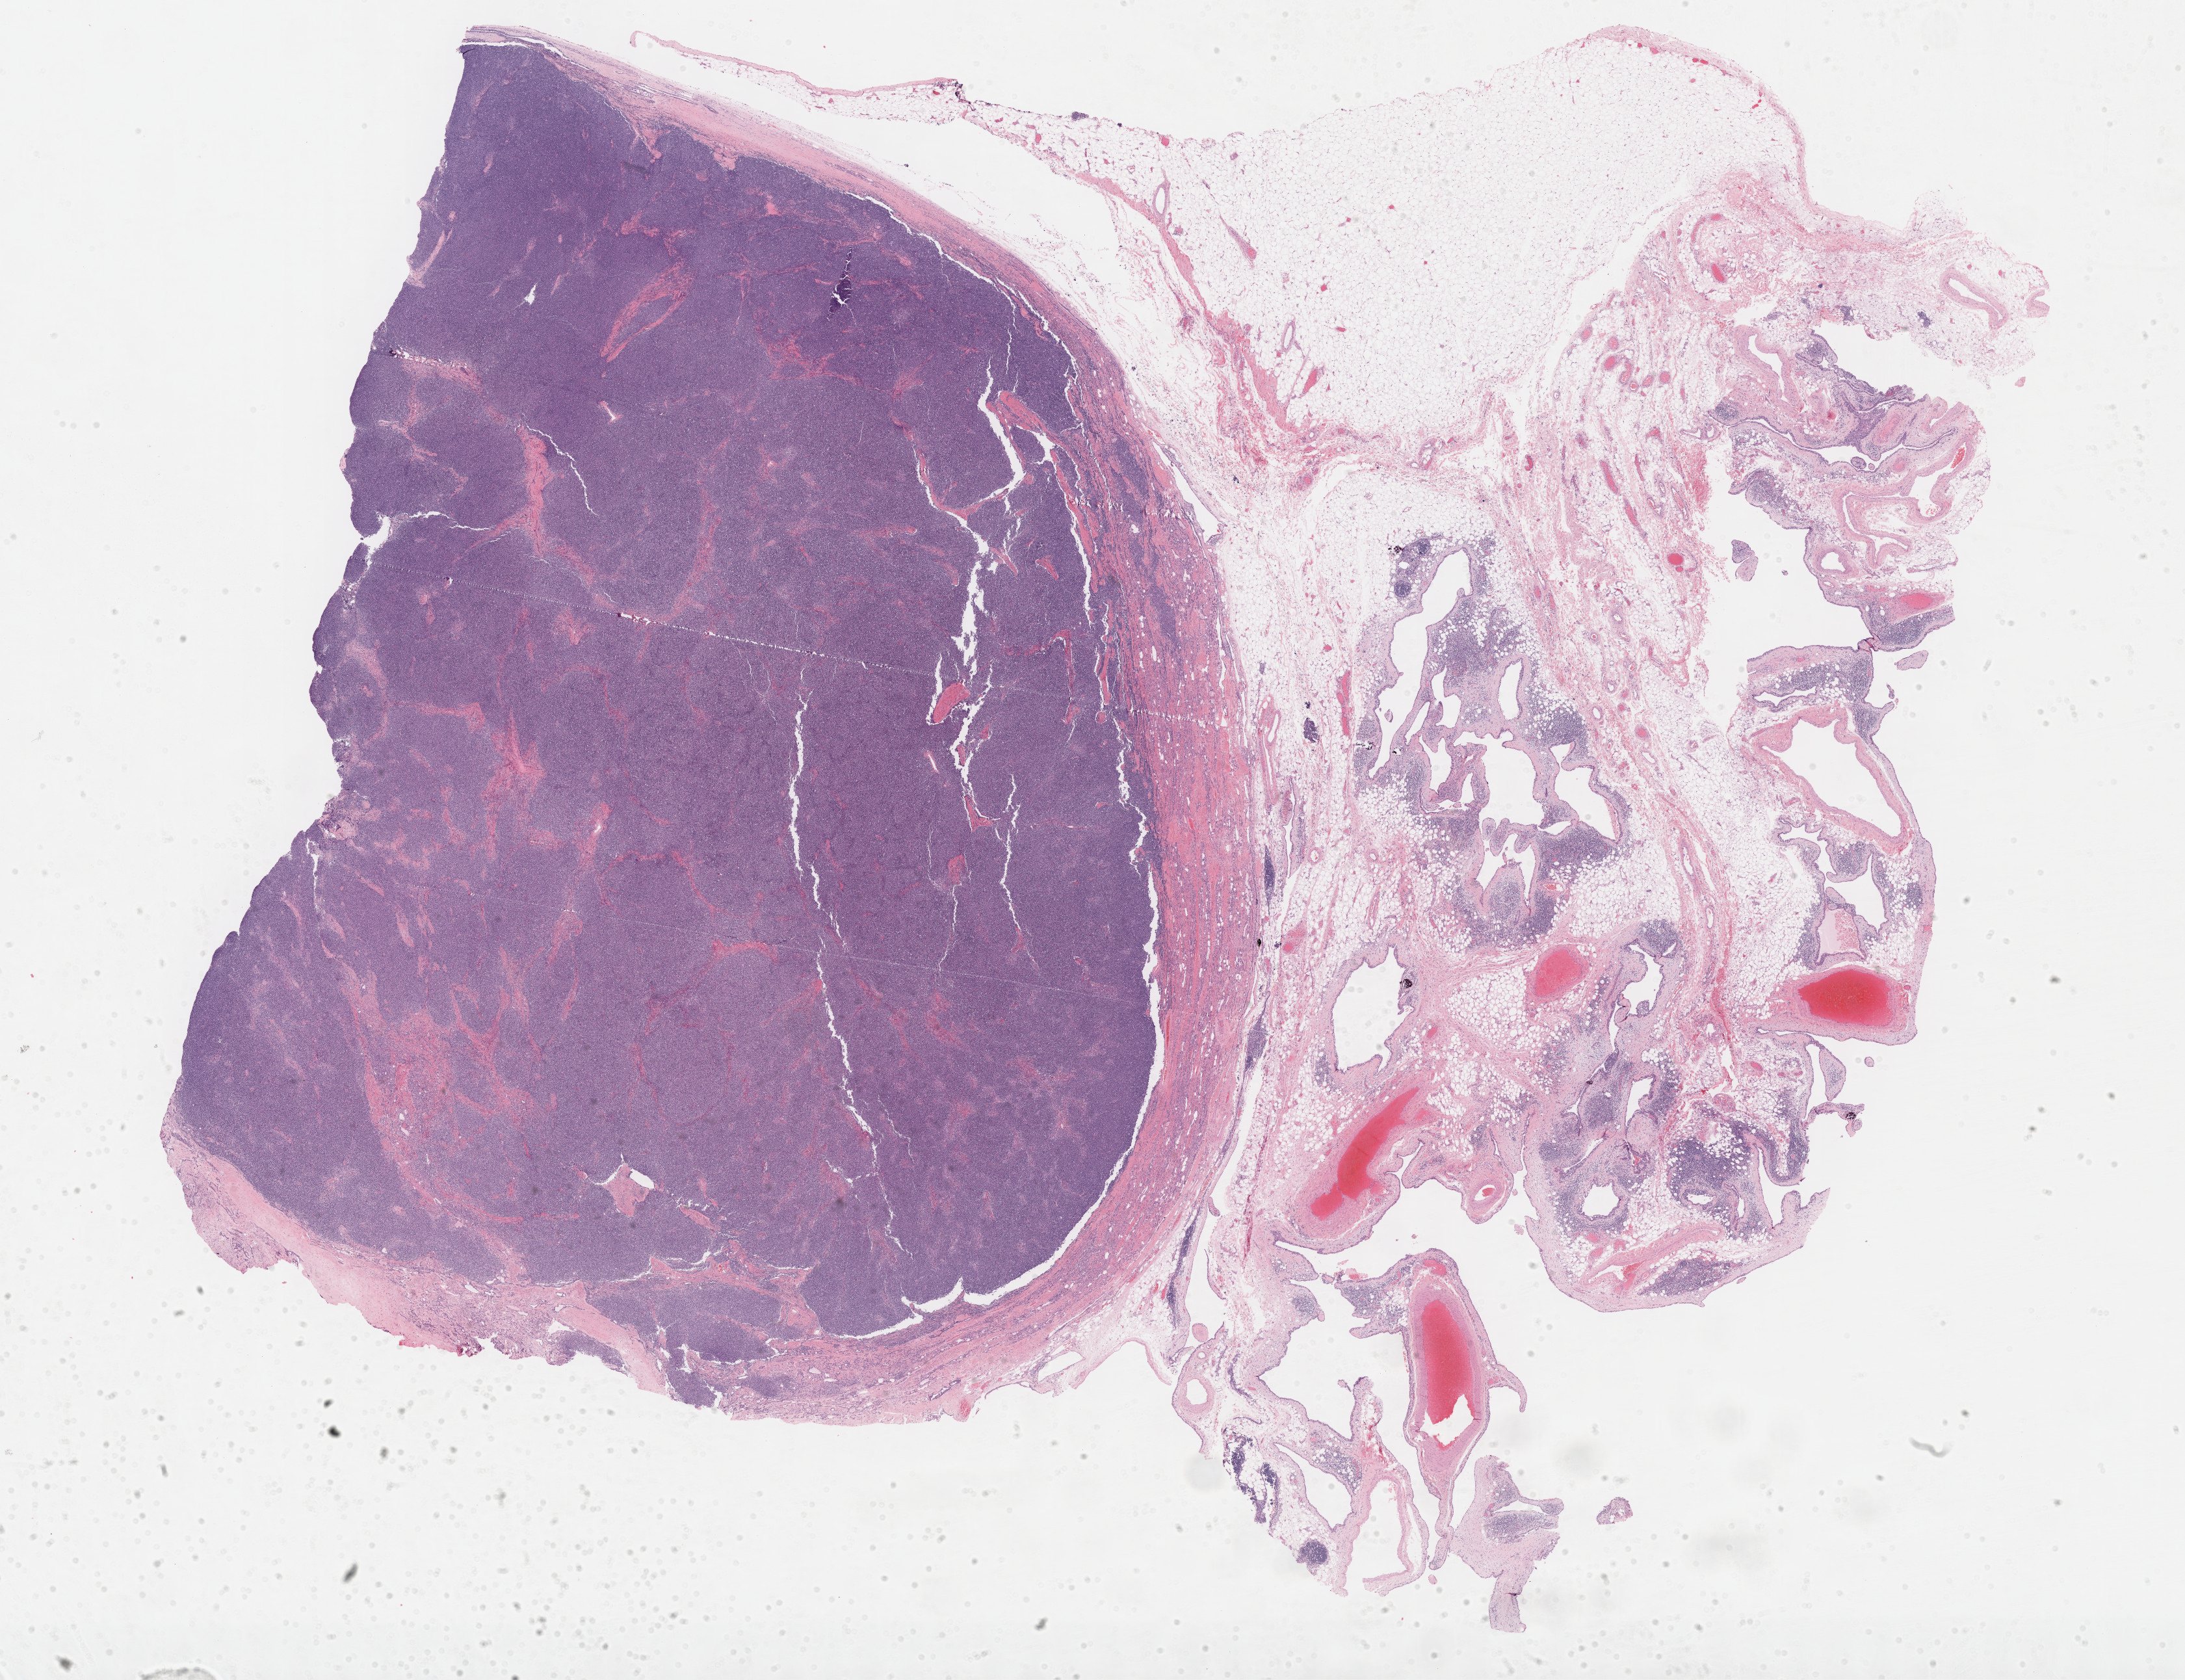
Whole-slide histology image, Hematoxylin and eosin (H&E) stained, a low-resolution overview of the entire scanned area, about 27.2 x 20.9 mm (acquisition: 40x scan), formalin-fixed paraffin-embedded (FFPE) diagnostic section, thymus, primary tumour sample. Male patient; age at initial diagnosis 51 years.
• diagnosis: Thymoma, type AB, NOS